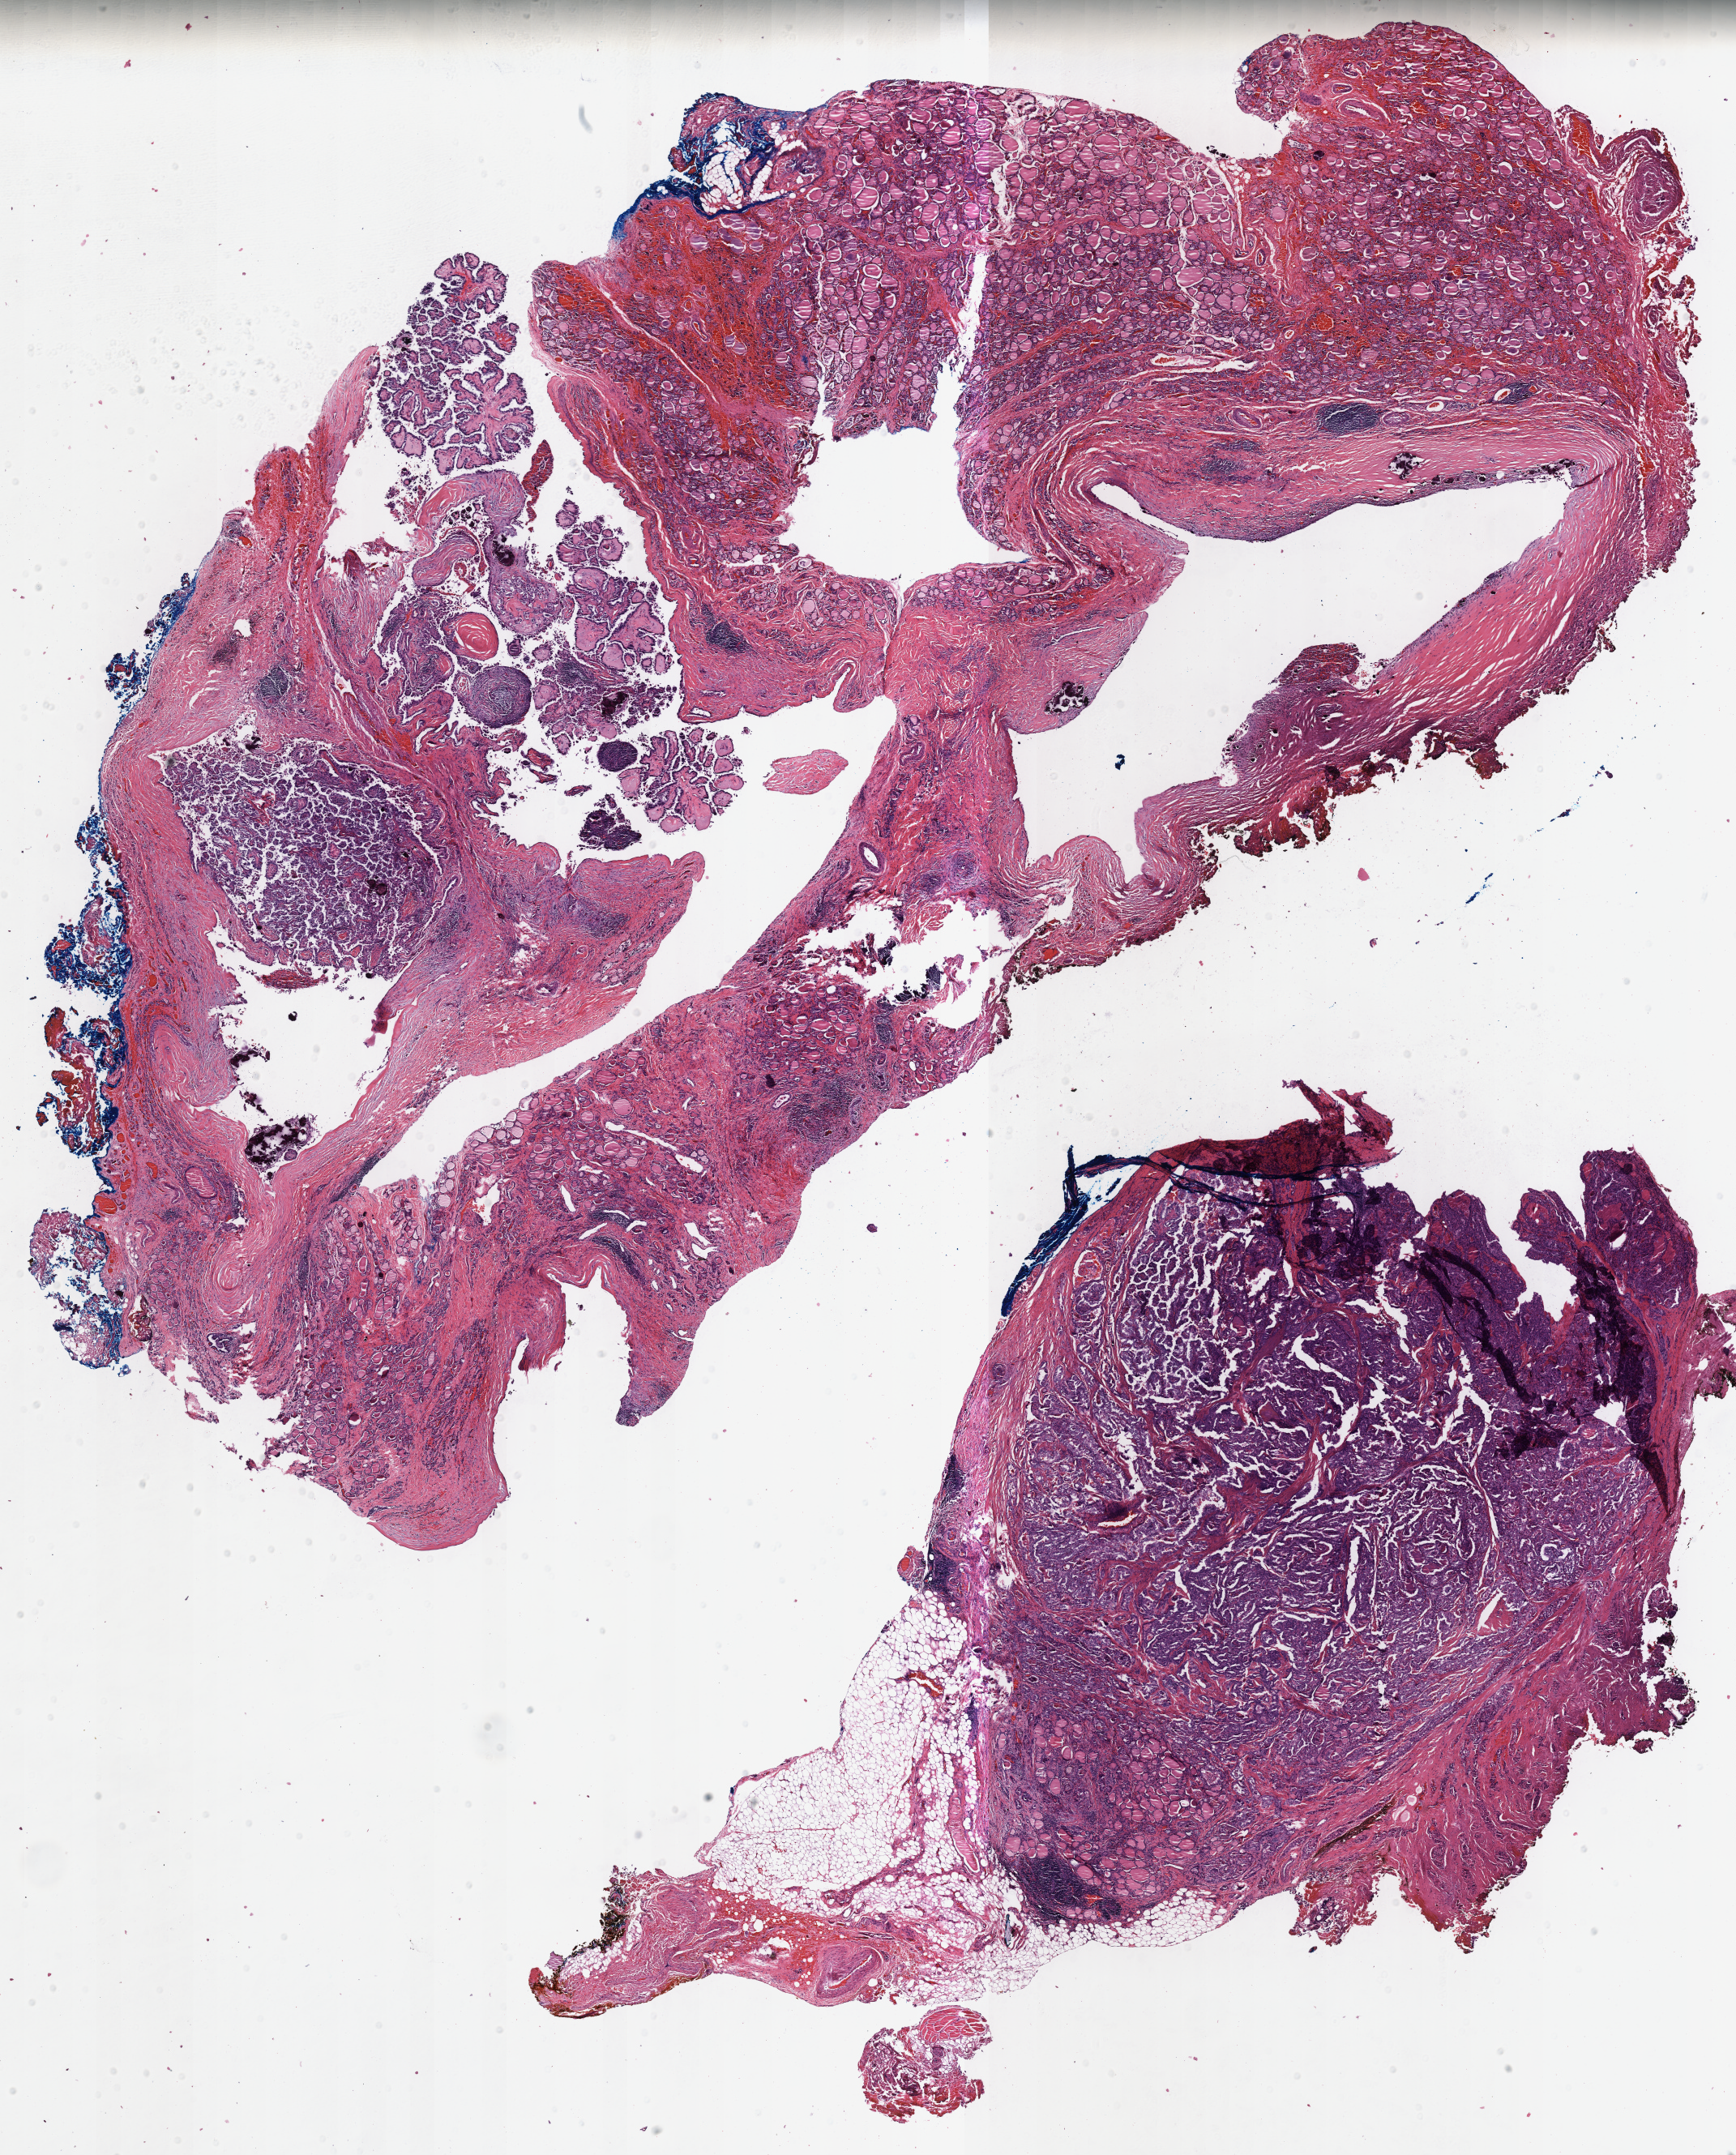
Hematoxylin and eosin (H&E) stained whole-slide image, shown as a low-resolution overview of the whole scanned area (about 16.9 x 20.9 mm, from a 40x scan). Formalin-fixed paraffin-embedded (FFPE) diagnostic section. Primary tumour sample from the thyroid. Female, age 62 years at initial diagnosis.
Laterality: right. Lymph nodes positive (case pathology): 2 of 3 examined. TNM: T1b N1a MX. Histologic diagnosis: Papillary adenocarcinoma, NOS (thyroid gland). AJCC pathologic stage: III (7th edition).